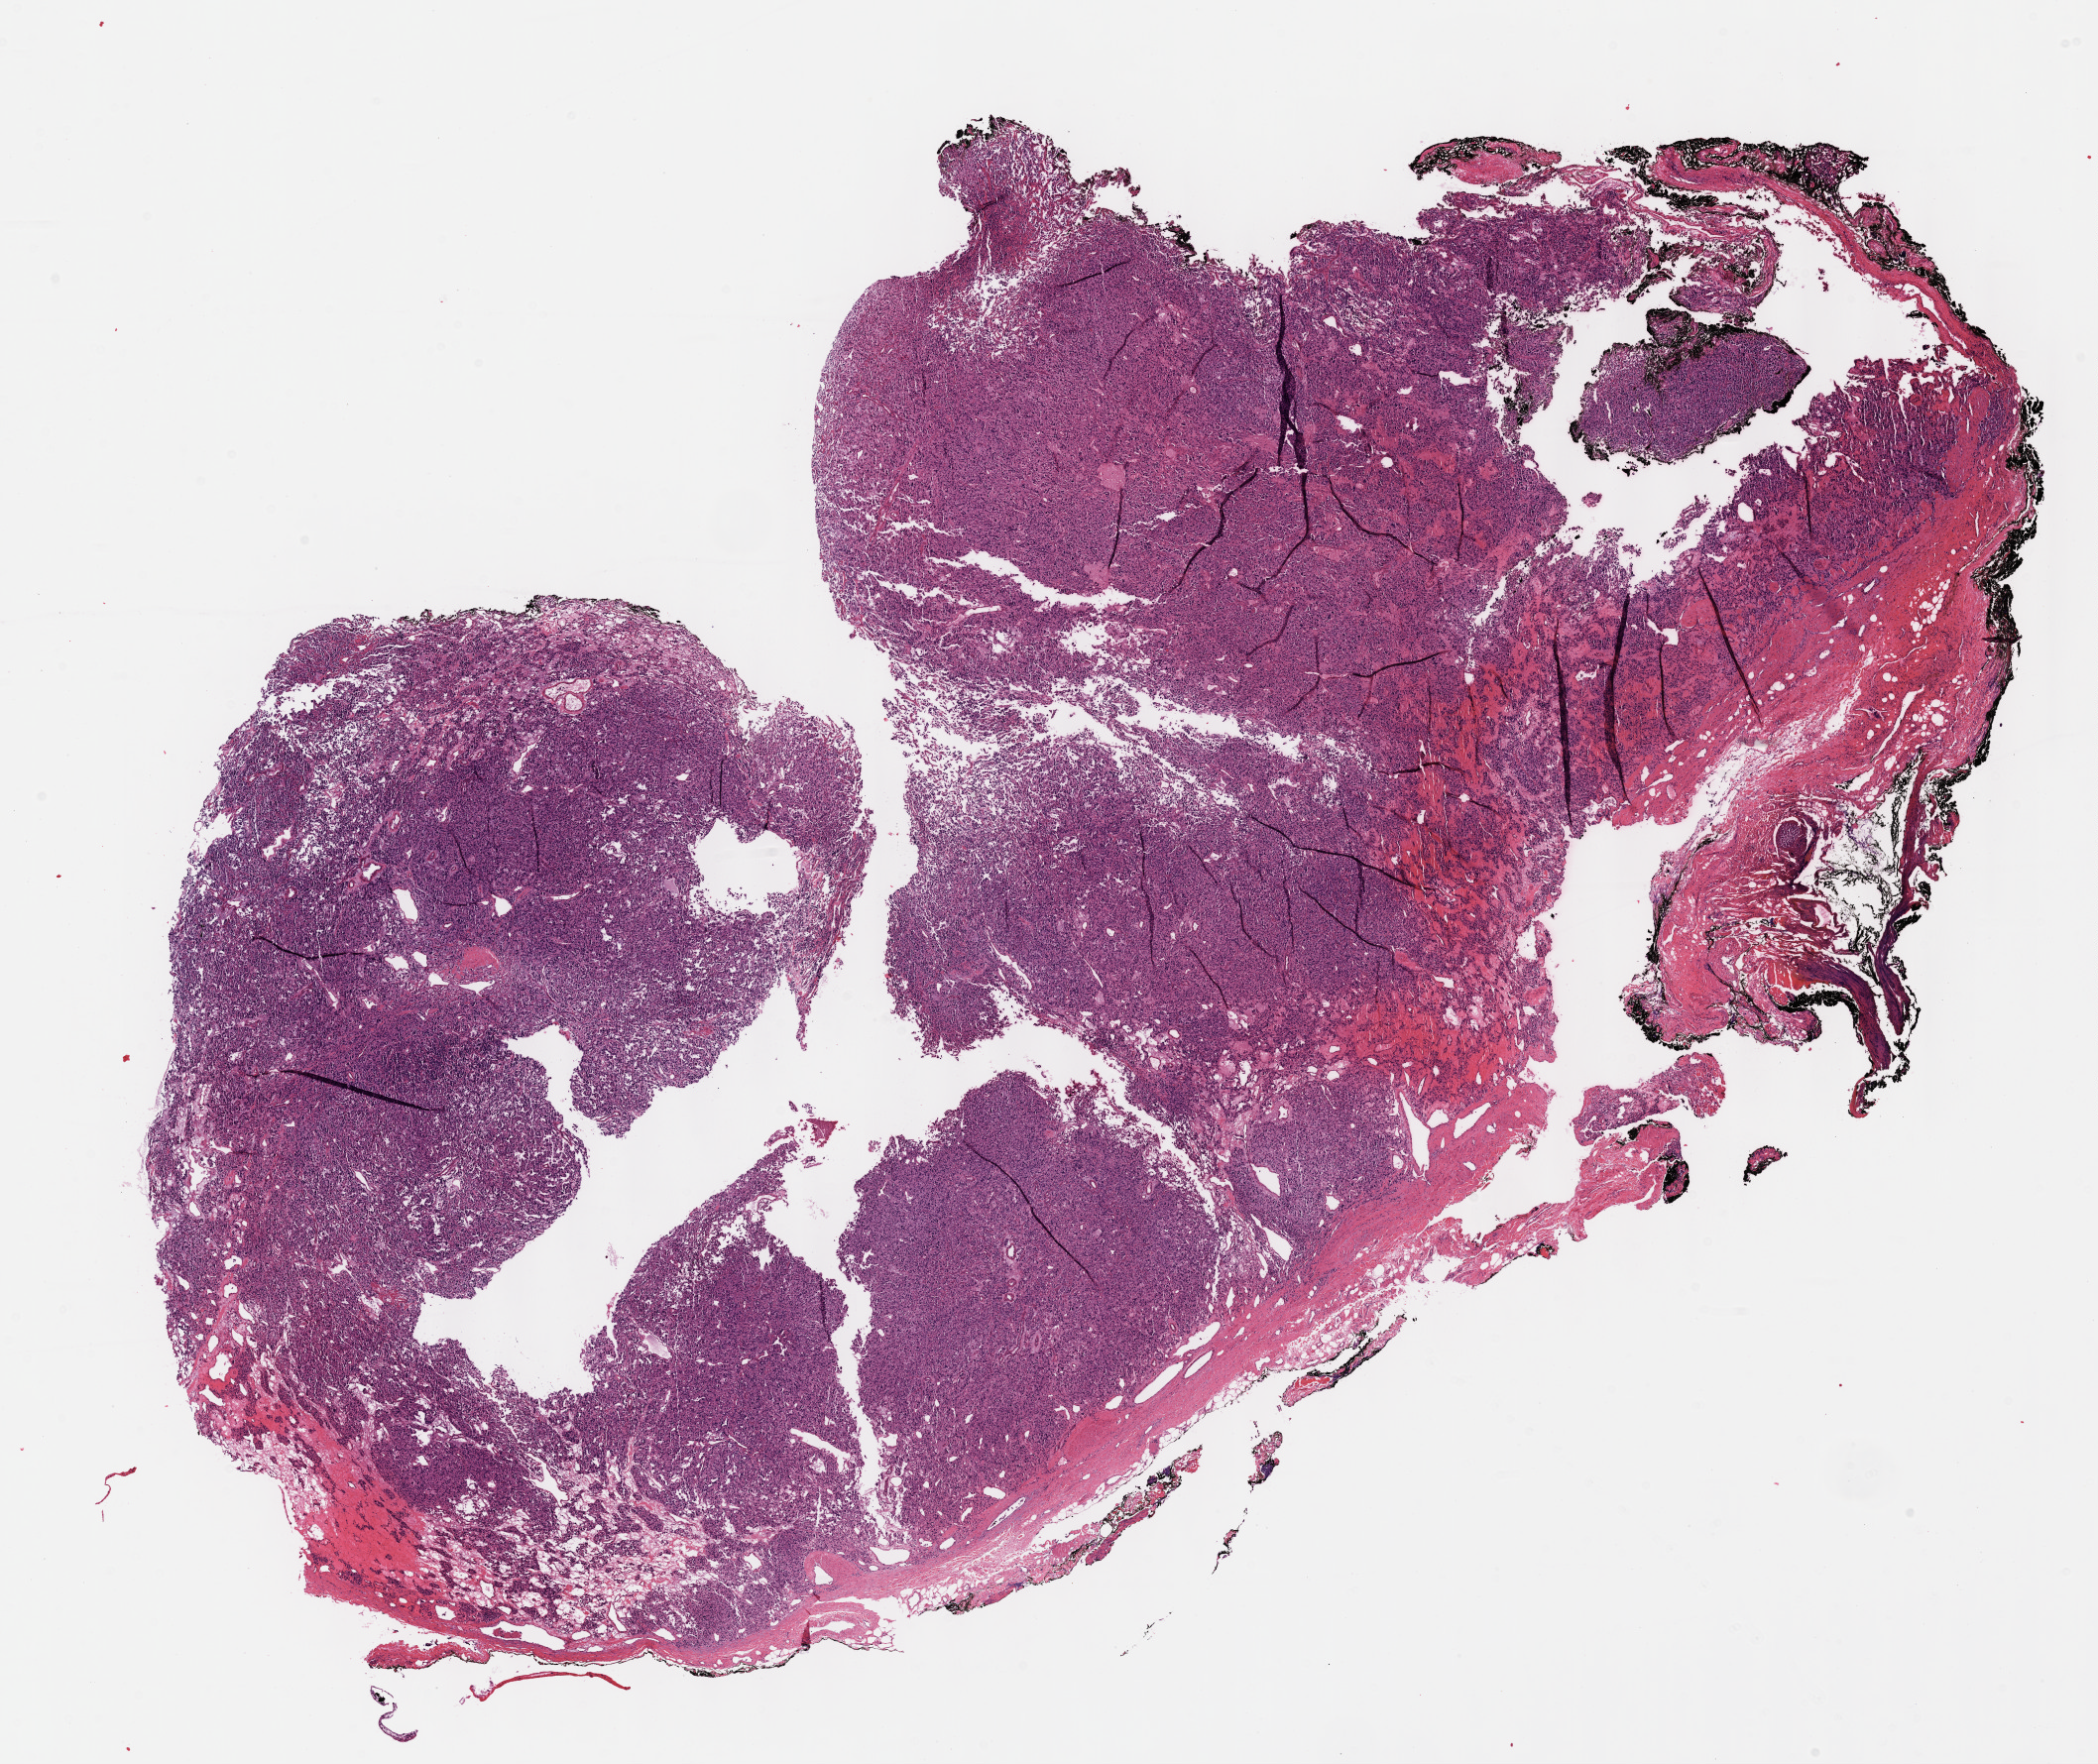
Whole-slide histology image, H&E-stained, shown as a low-resolution overview of the whole scanned area (about 17.1 x 14.4 mm). FFPE section. Sample: primary tumour, connective, subcutaneous and other soft tissues. Patient: male, age at initial diagnosis 61 years.
Histologic diagnosis: Extra-adrenal paraganglioma, NOS (connective, subcutaneous and other soft tissues of abdomen). Lymph nodes positive (case pathology): 0 of 1 examined.